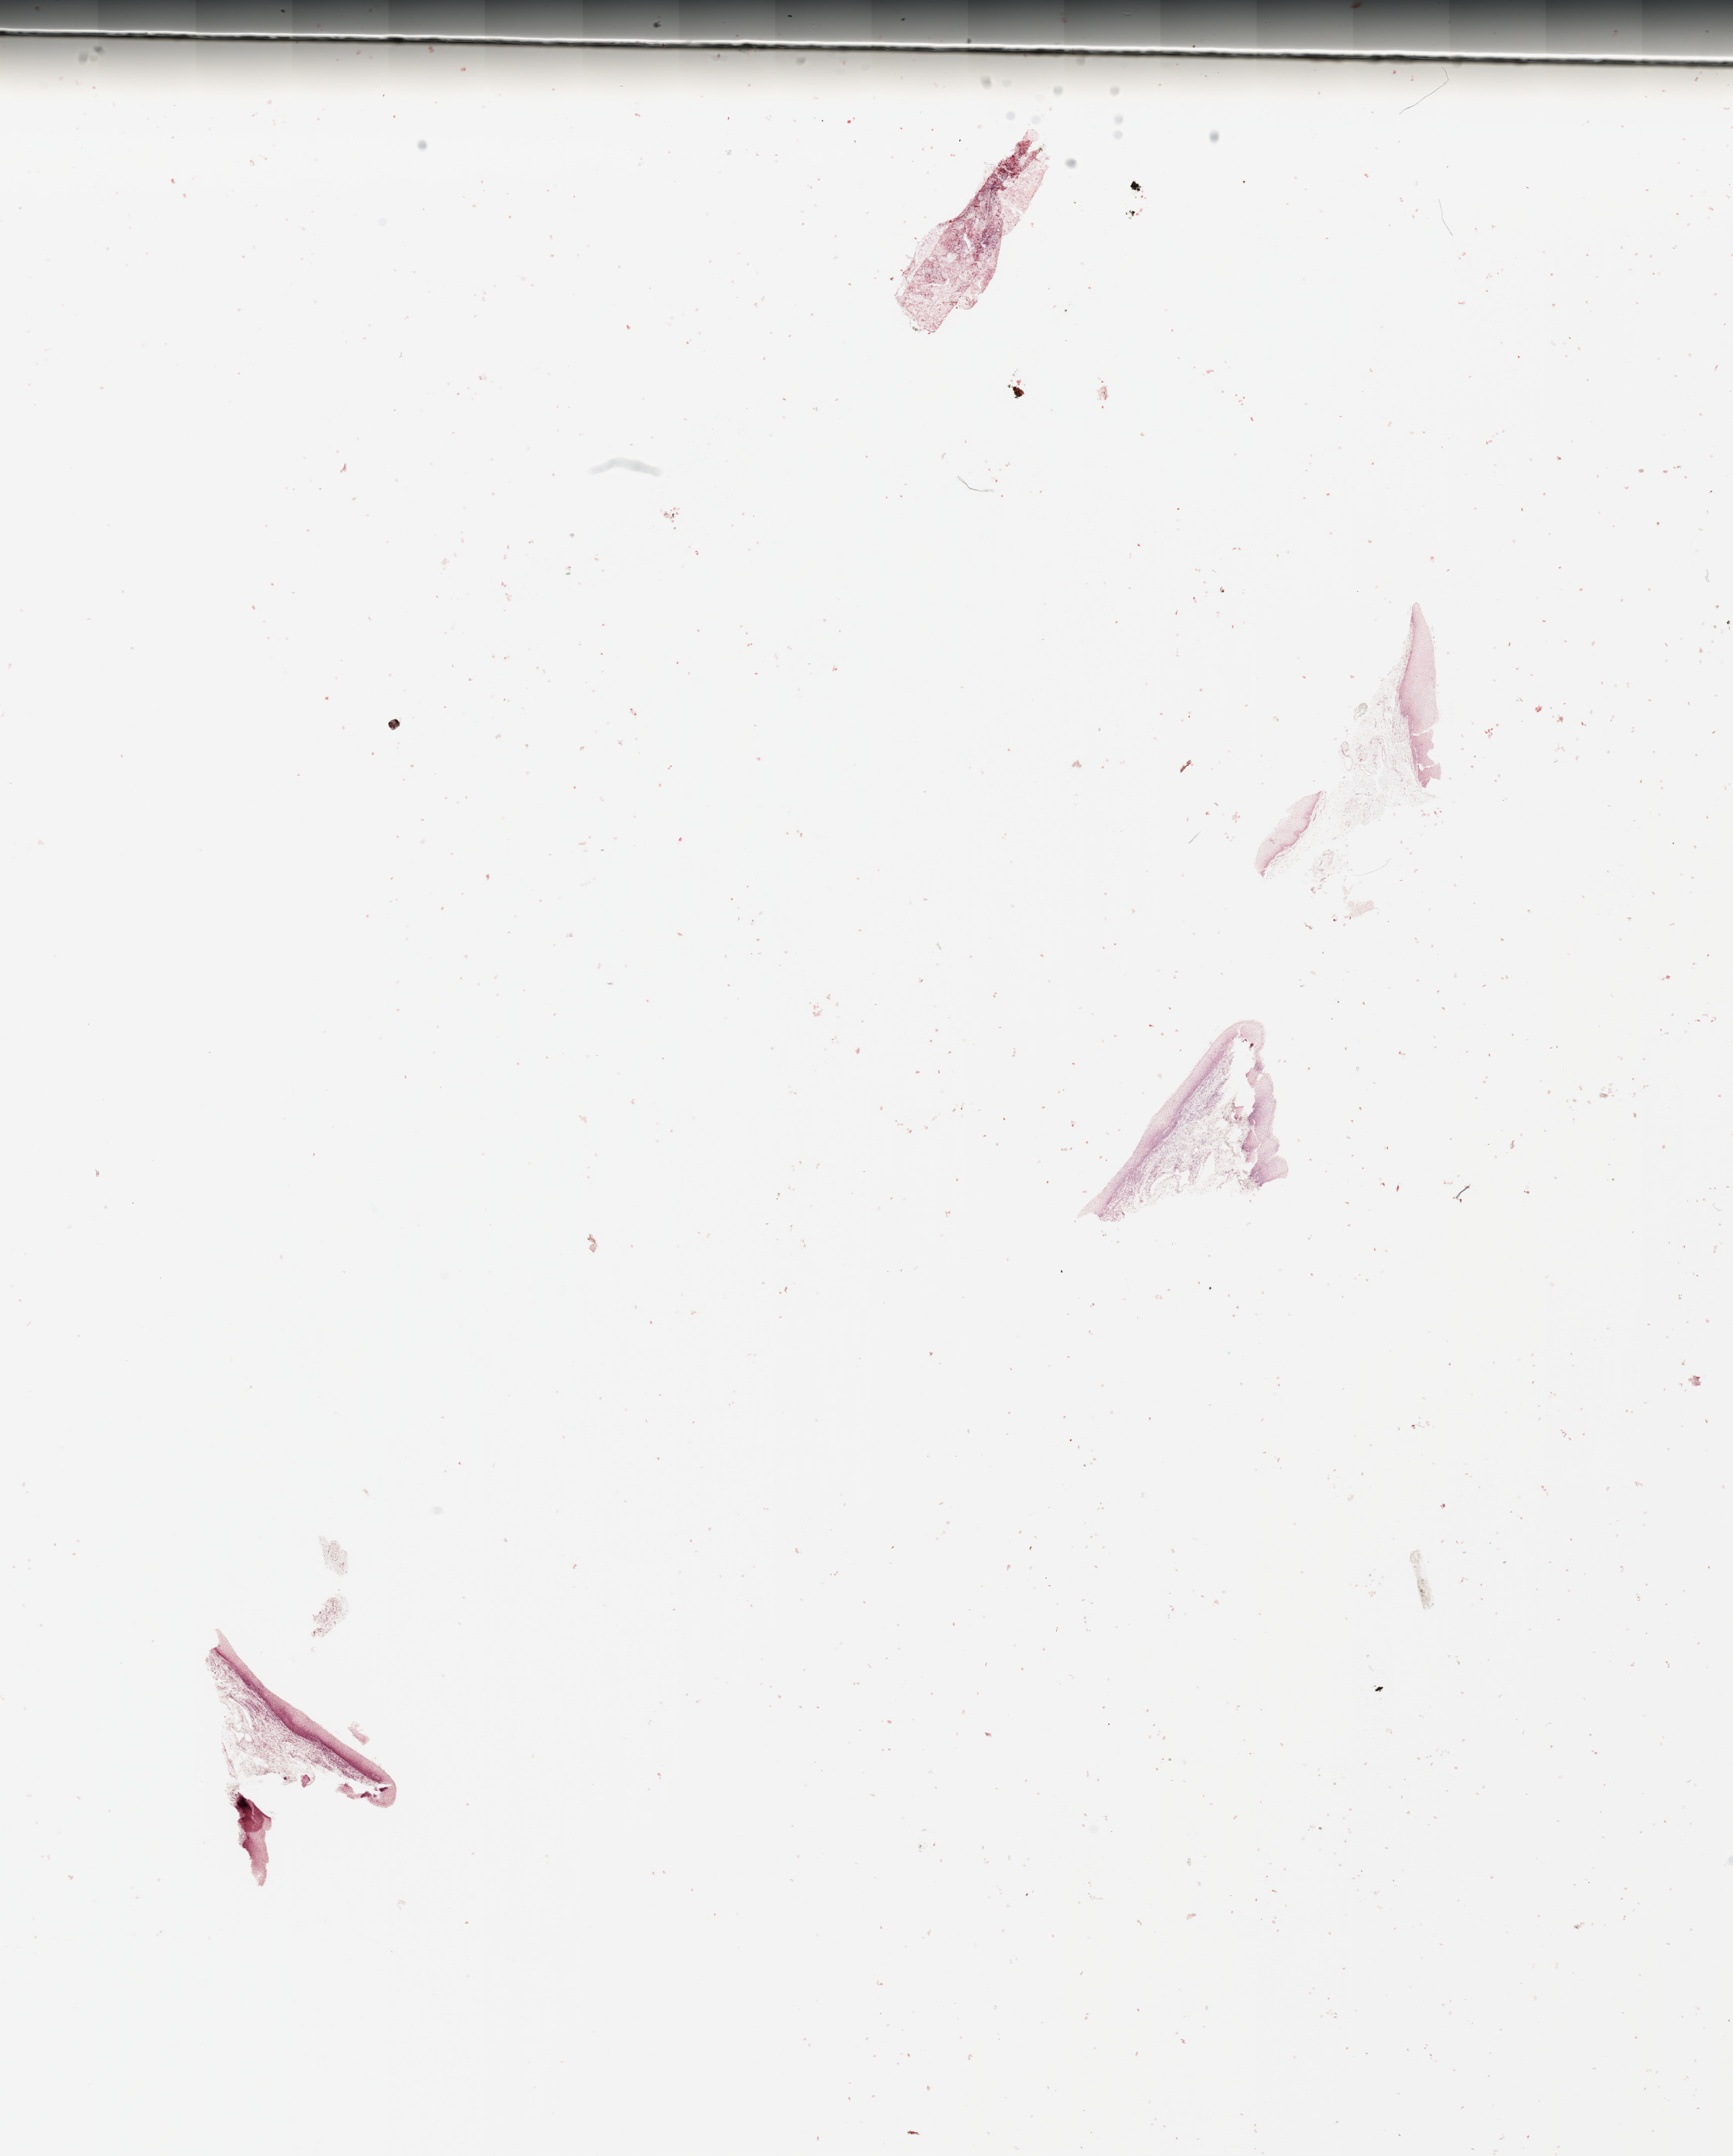
Hematoxylin and eosin (H&E) stained whole-slide image, a low-resolution overview of the entire scanned area, about 17.7 x 22.0 mm, normal (non-tumour) tissue sample, head and neck. Patient: male, age 64 years.
This section: normal (non-tumour) tissue from the same patient. Patient diagnosis: Squamous cell carcinoma, NOS.